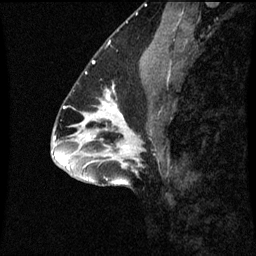
Breast MRI (dynamic contrast-enhanced), one sagittal slice. Position 35 of 60 along the scan axis. Dynamic contrast-enhanced series, image 2 of 3 at this slice position (ordered by acquisition). 1.5 T. TE 4.2 ms, TR 8.9 ms. 2 mm slice thickness. 256 × 256 image matrix, field of view 200 × 200 mm. Female patient, age 43 years. Case-level facts recorded for this patient, not image findings: setting: breast cancer imaged before/during neoadjuvant chemotherapy; receptor status: HR-positive, HER2-negative.
Outlined on this slice (semi-automatic segmentation, software-assisted and operator-edited):
- analysis volume of interest (the breast-tissue region the enhancement analysis was run in; not a lesion): box from (x=96, y=96) to (x=155, y=159) px
- tumour enhancement mask (voxels above the 70 % enhancement threshold inside the analysis volume of interest): (x=104, y=96)–(x=123, y=117)